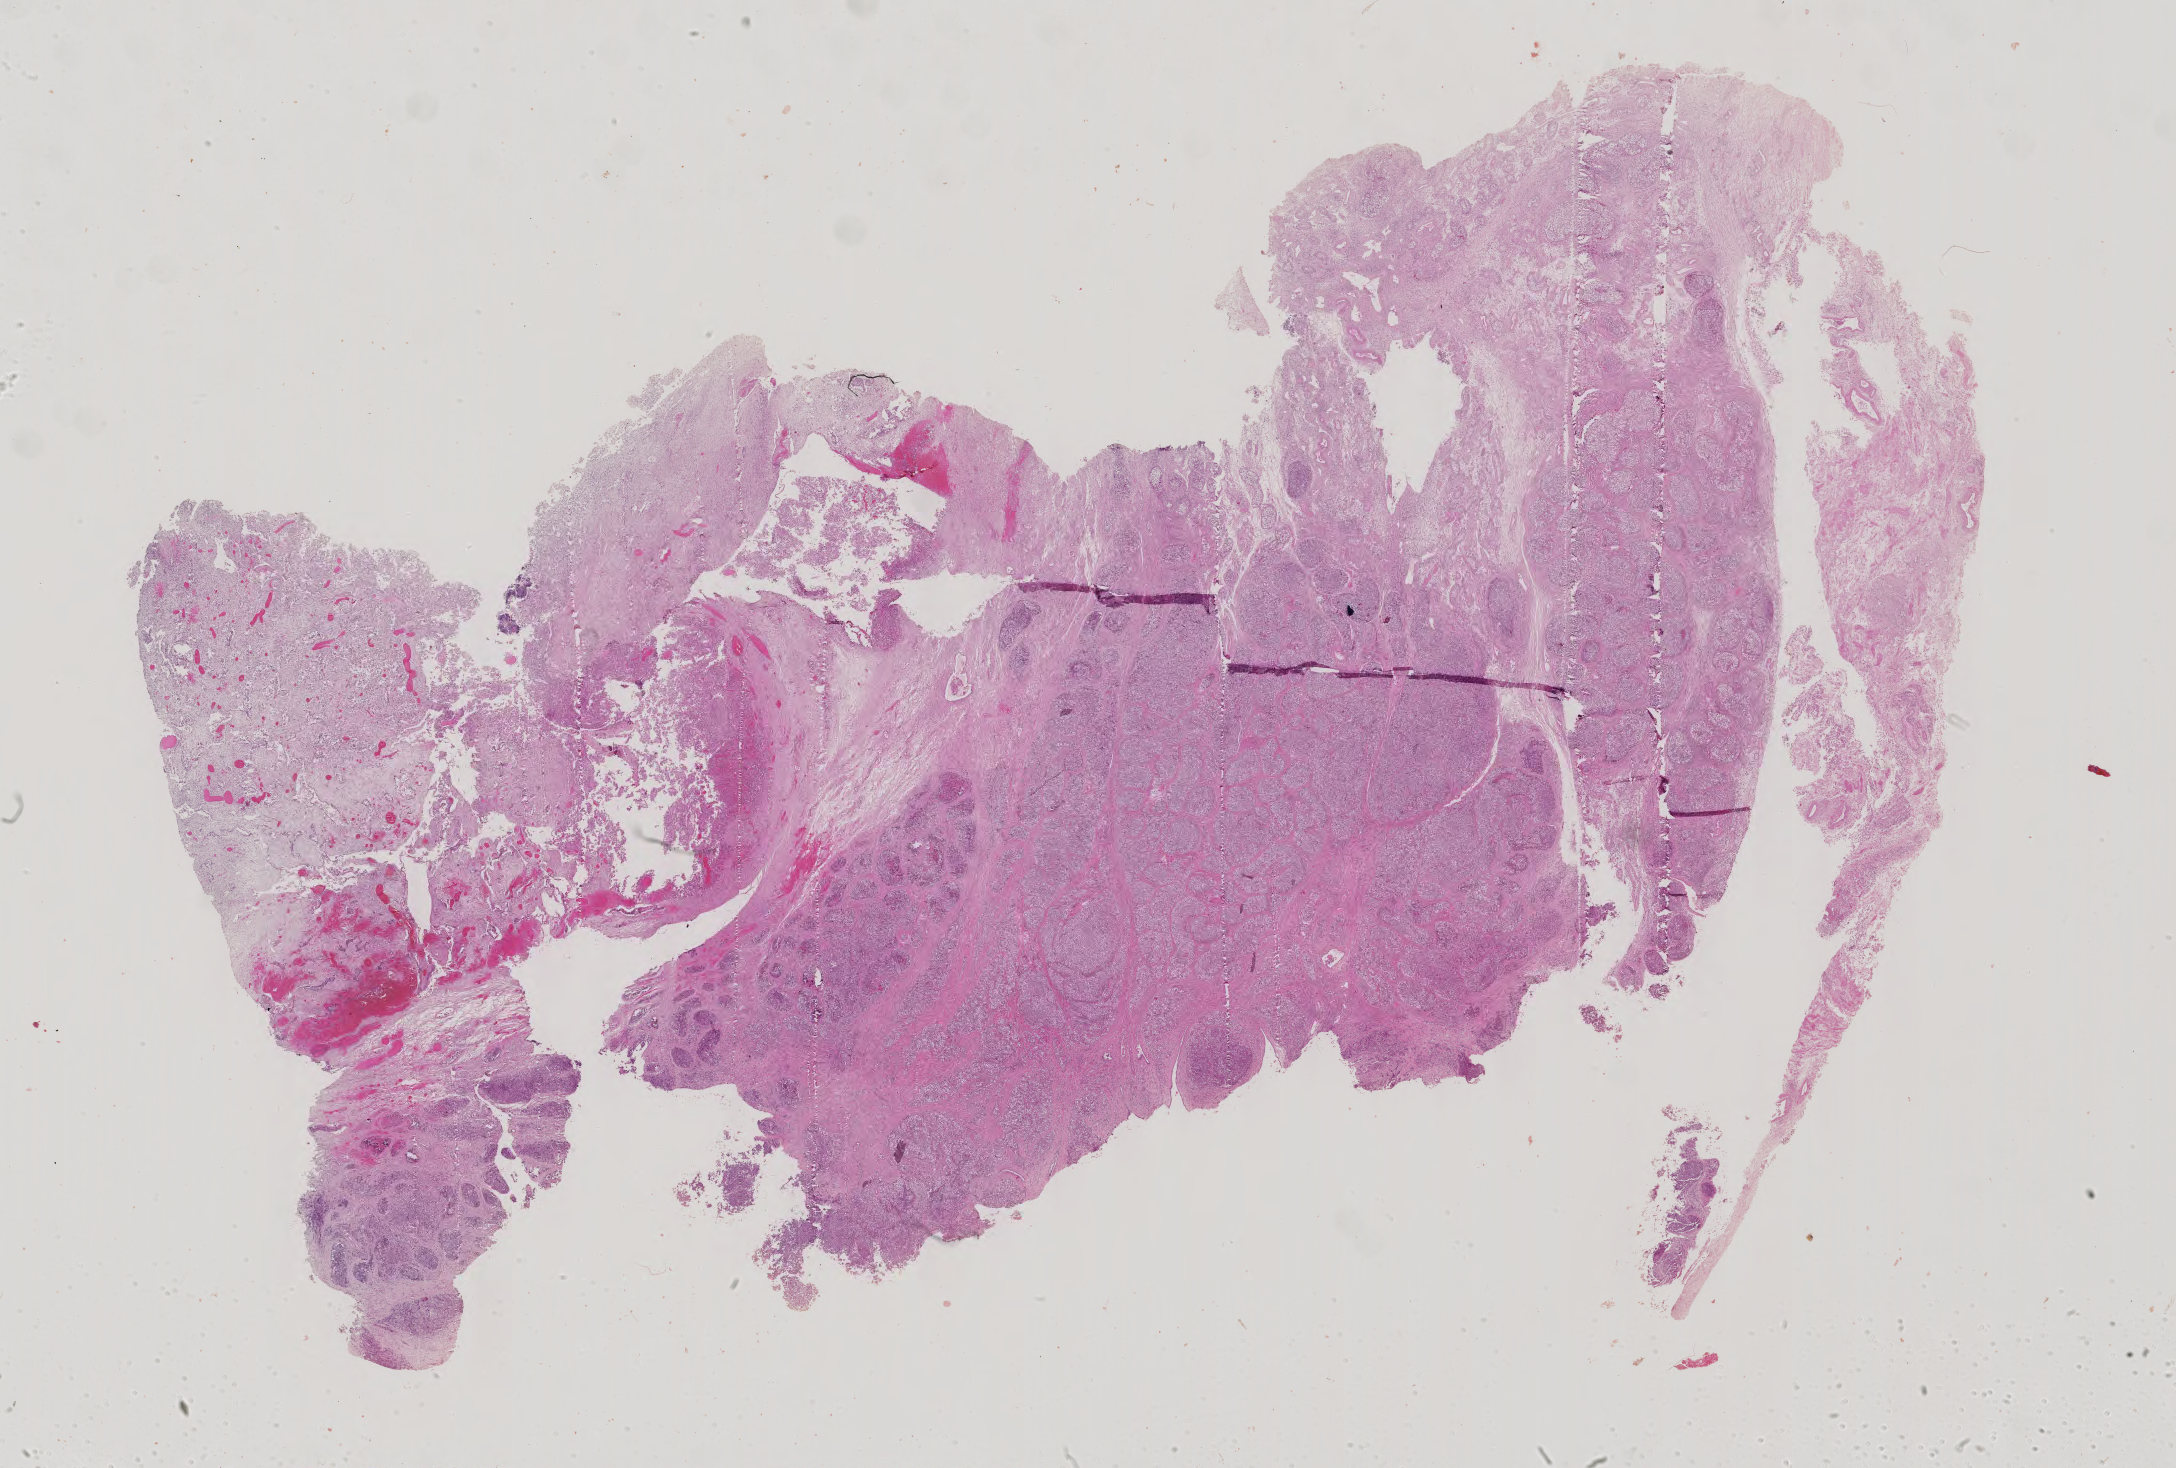
Whole-slide histology image, Hematoxylin and eosin (H&E) stained, whole scanned area (about 31.7 x 21.4 mm, slide scanned at 40x) shown as a low-resolution overview, FFPE section, testis, primary tumour sample. Patient: male, age at initial diagnosis 20 years.
AJCC pathologic stage: I (4th edition). Histologic diagnosis: Seminoma, NOS.